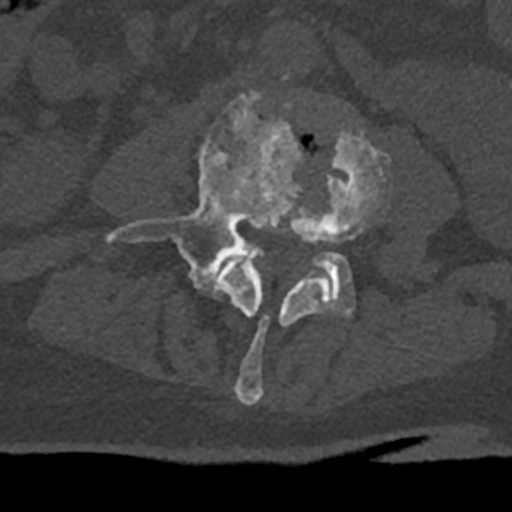
CT including the spine, one axial slice. Reconstruction kernel Br40s/3. Bone window (W 1800 / L 400 HU). 0.5 mm slice thickness. 512 × 512 image matrix, field of view 160 × 160 mm. Patient: male, 74 years. Case-level facts recorded for this patient, not image findings: primary cancer: renal; vertebrae with lytic lesions (as recorded): T10, L1, L2, L3, L4, L5.
Outlined on this slice (semi-automatically segmented with operator editing):
- L3 vertebra: bounding box [x1, y1, x2, y2] px = [216, 129, 389, 405]
- L4 vertebra: [106, 92, 354, 317]